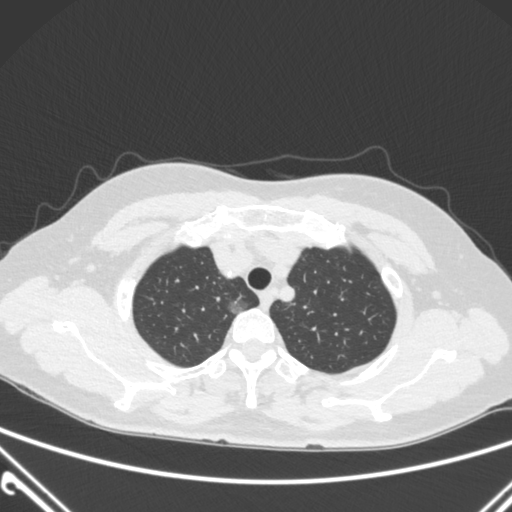
Chest CT, one axial slice. Position 239 of 300 along the scan axis. Lung window (W 1500 / L -600 HU). 512 × 512 image matrix. Patient: female, 54 years. From the clinical record (not read from this slice): clinical TNM (as recorded): T1a N0 M0; histopathological grade: G1.
Structures marked on this image (rectangle marked by the reading radiologist):
- lung tumour (recorded histology: adenocarcinoma): box from (x=222, y=289) to (x=259, y=328) px